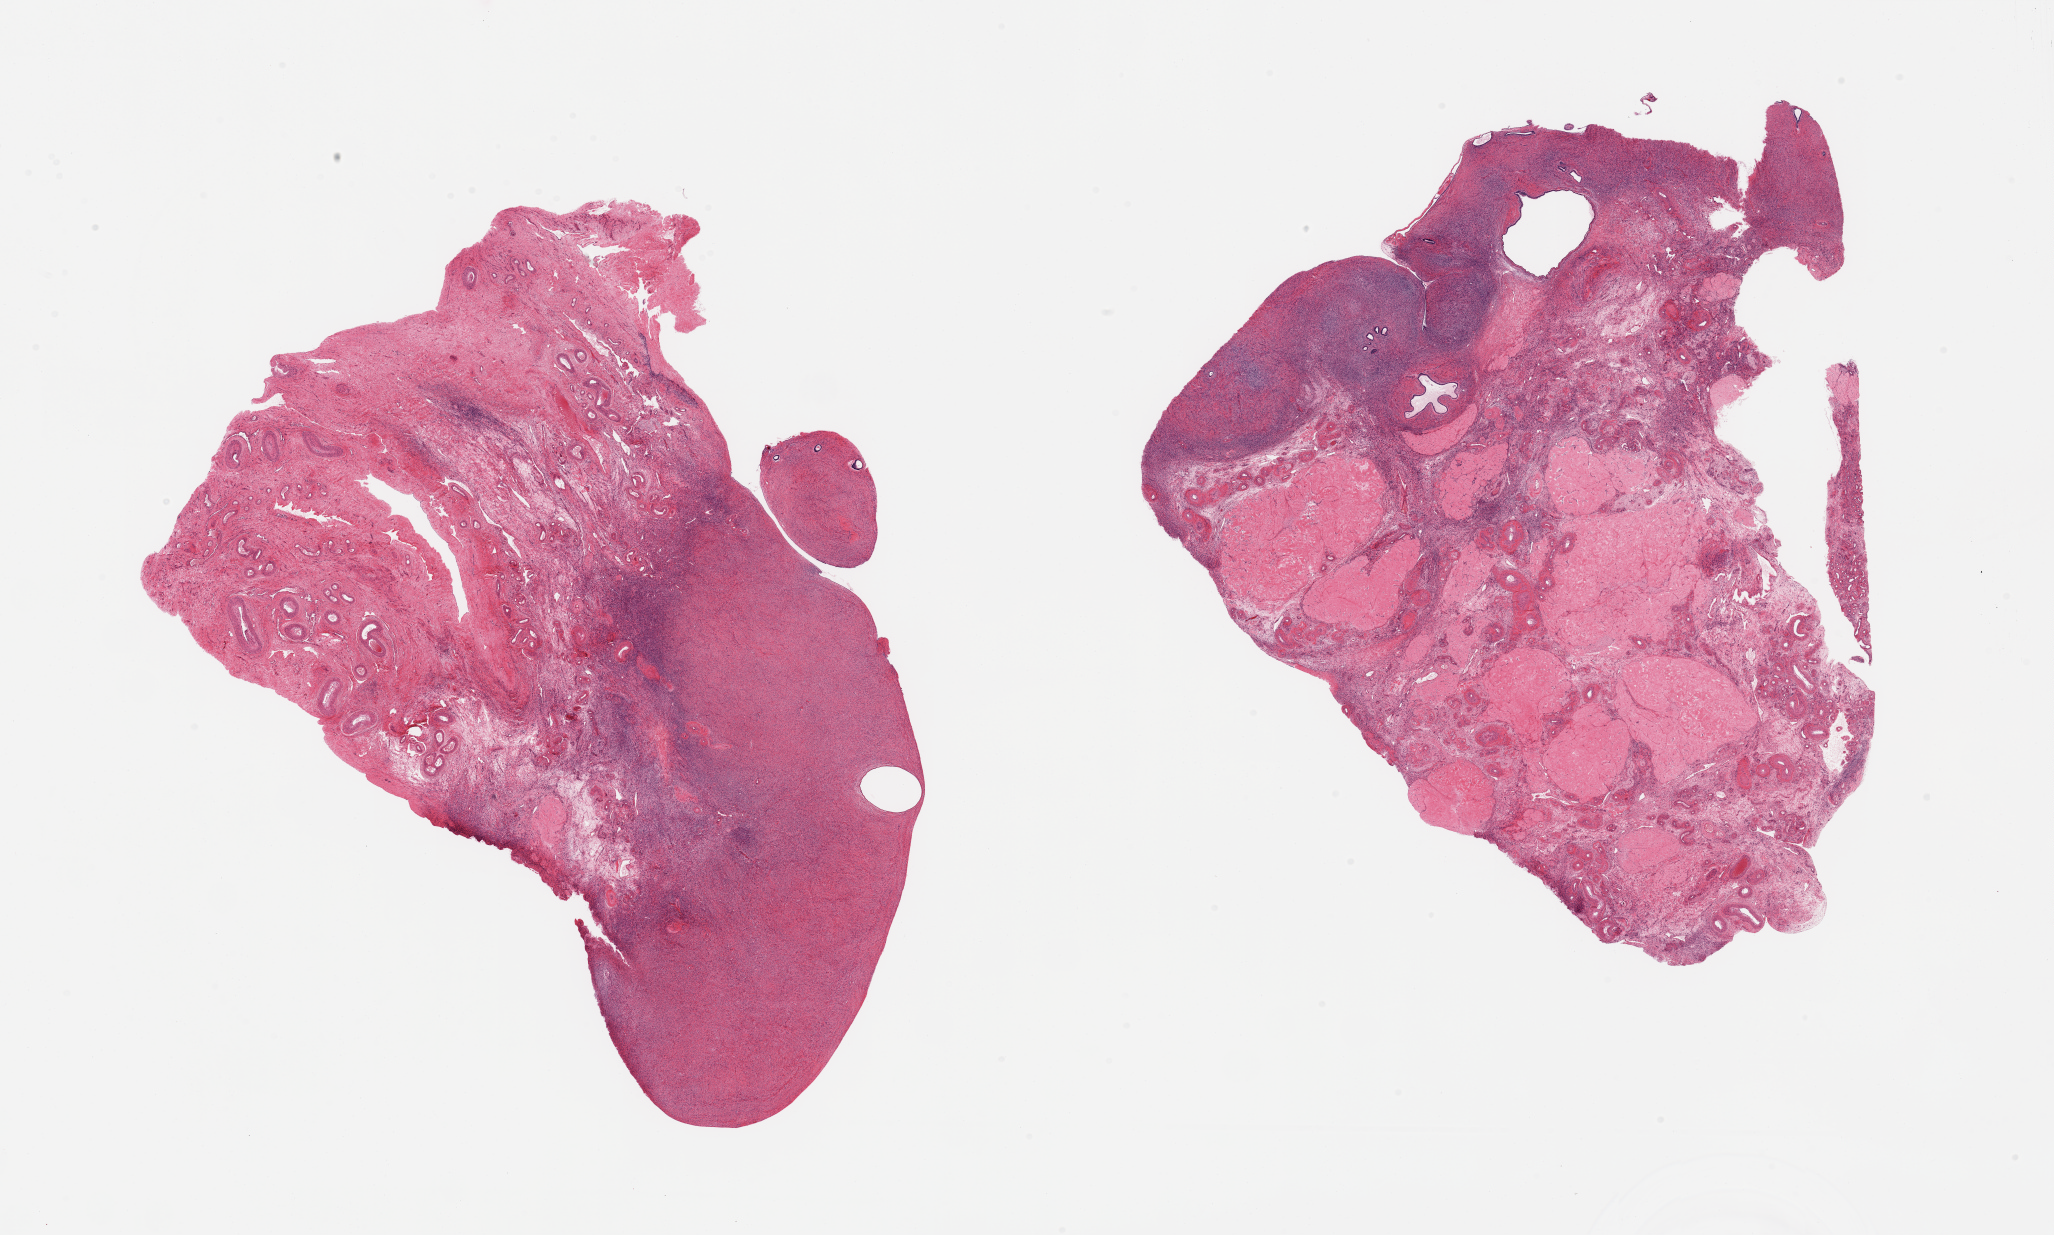
Whole-slide image, haematoxylin and eosin stain — low-resolution overview of the scanned area, about 32.5 x 19.5 mm. PAXgene-fixed, paraffin-embedded tissue. Sampled site (target tissue): ovary. Donor tissue sample. Female donor.
Pathologist's review note for this sample: 2 pieces, small simple cyst; corpora albicantia; Typical post menopausal changes.